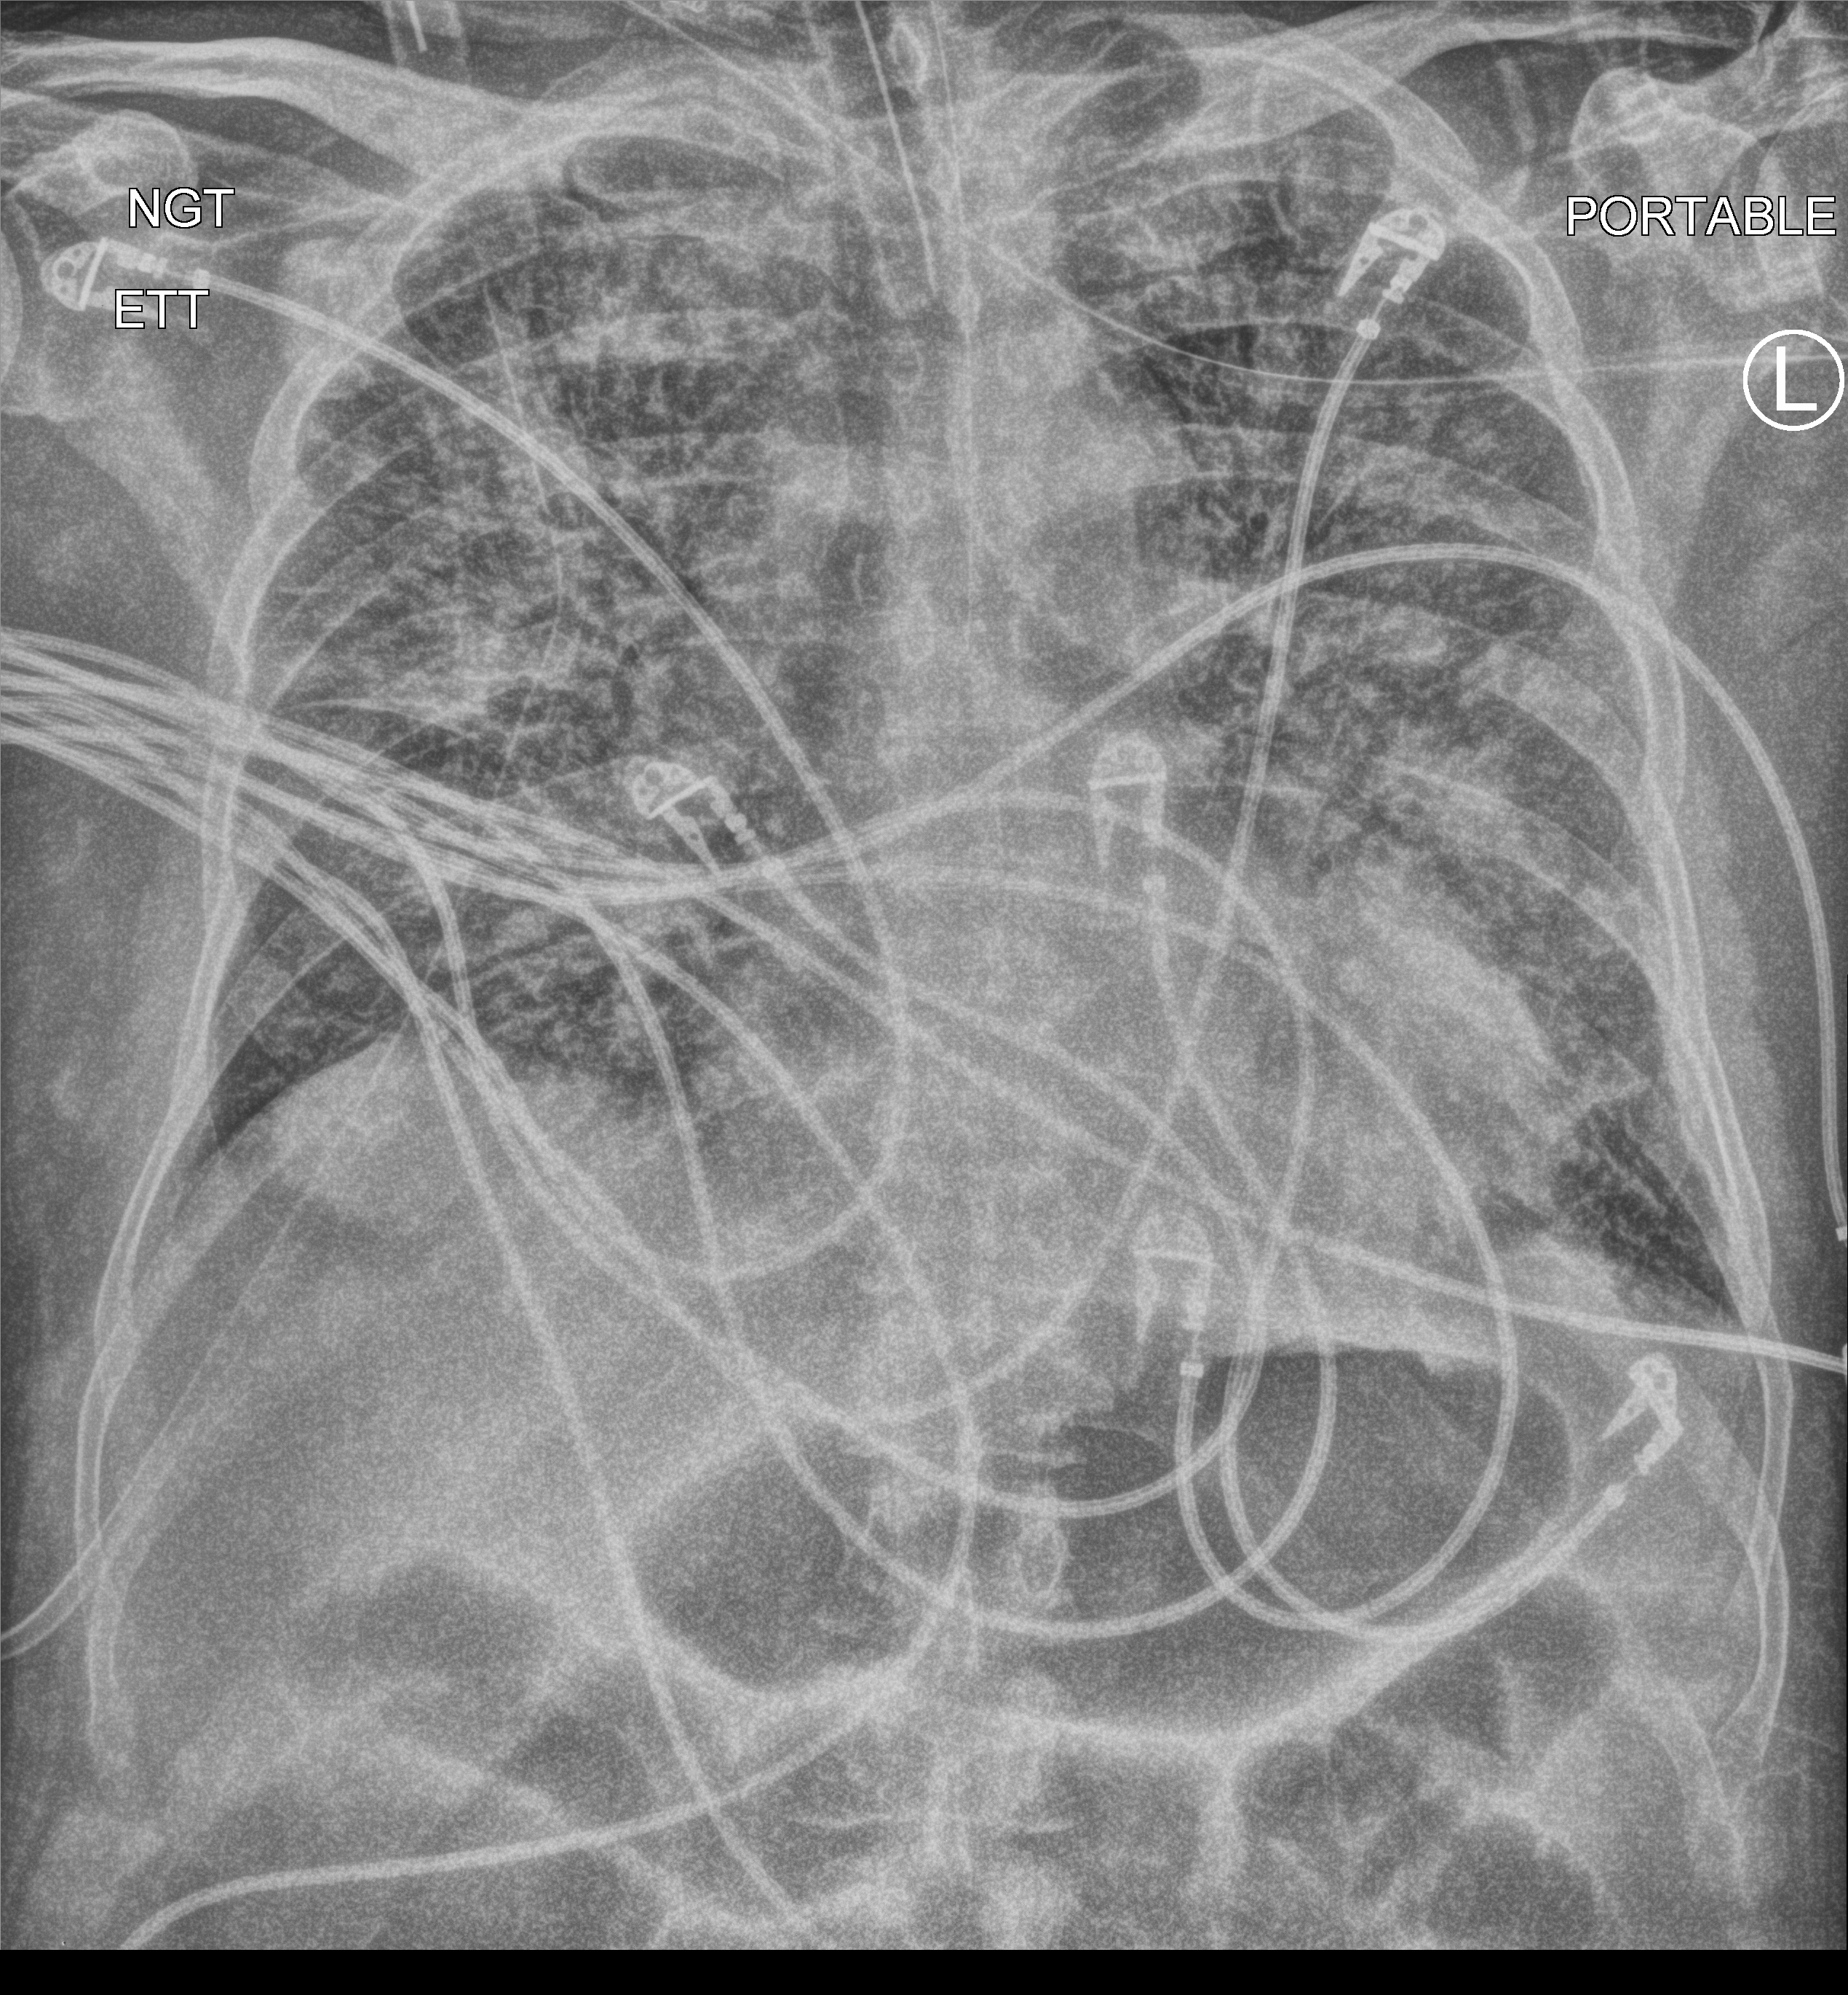
Chest X-ray (portable). Patient hospitalised with COVID-19; male, aged 60–74 years.
From the hospital-stay record, not from the radiograph (when in the stay this image was taken is not recorded): mechanically ventilated during this hospital stay: yes; admitted to intensive care during this hospital stay: yes; diabetes (admission record): no.